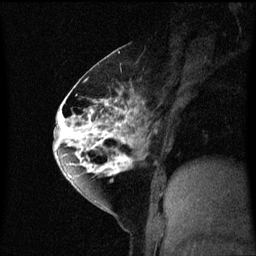
Breast MRI (dynamic contrast-enhanced), one sagittal slice; slice 30 of 60 in the series (ordered by position); dynamic contrast-enhanced series, image 2 of 3 at this slice position (ordered by acquisition); 1.5 T; TE 4.2 ms, TR 8.4 ms; 2 mm slice thickness; 256 × 256 image matrix, field of view 200 × 200 mm. Female patient, age 60 years.
Structures marked on this image (semi-automatically segmented with operator editing):
- analysis volume of interest (the breast-tissue region the enhancement analysis was run in; not a lesion): bounding box <64,70,141,195> (left, top, right, bottom; pixels)
- tumour enhancement mask (voxels above the 70 % enhancement threshold inside the analysis volume of interest): <64,80,141,187>